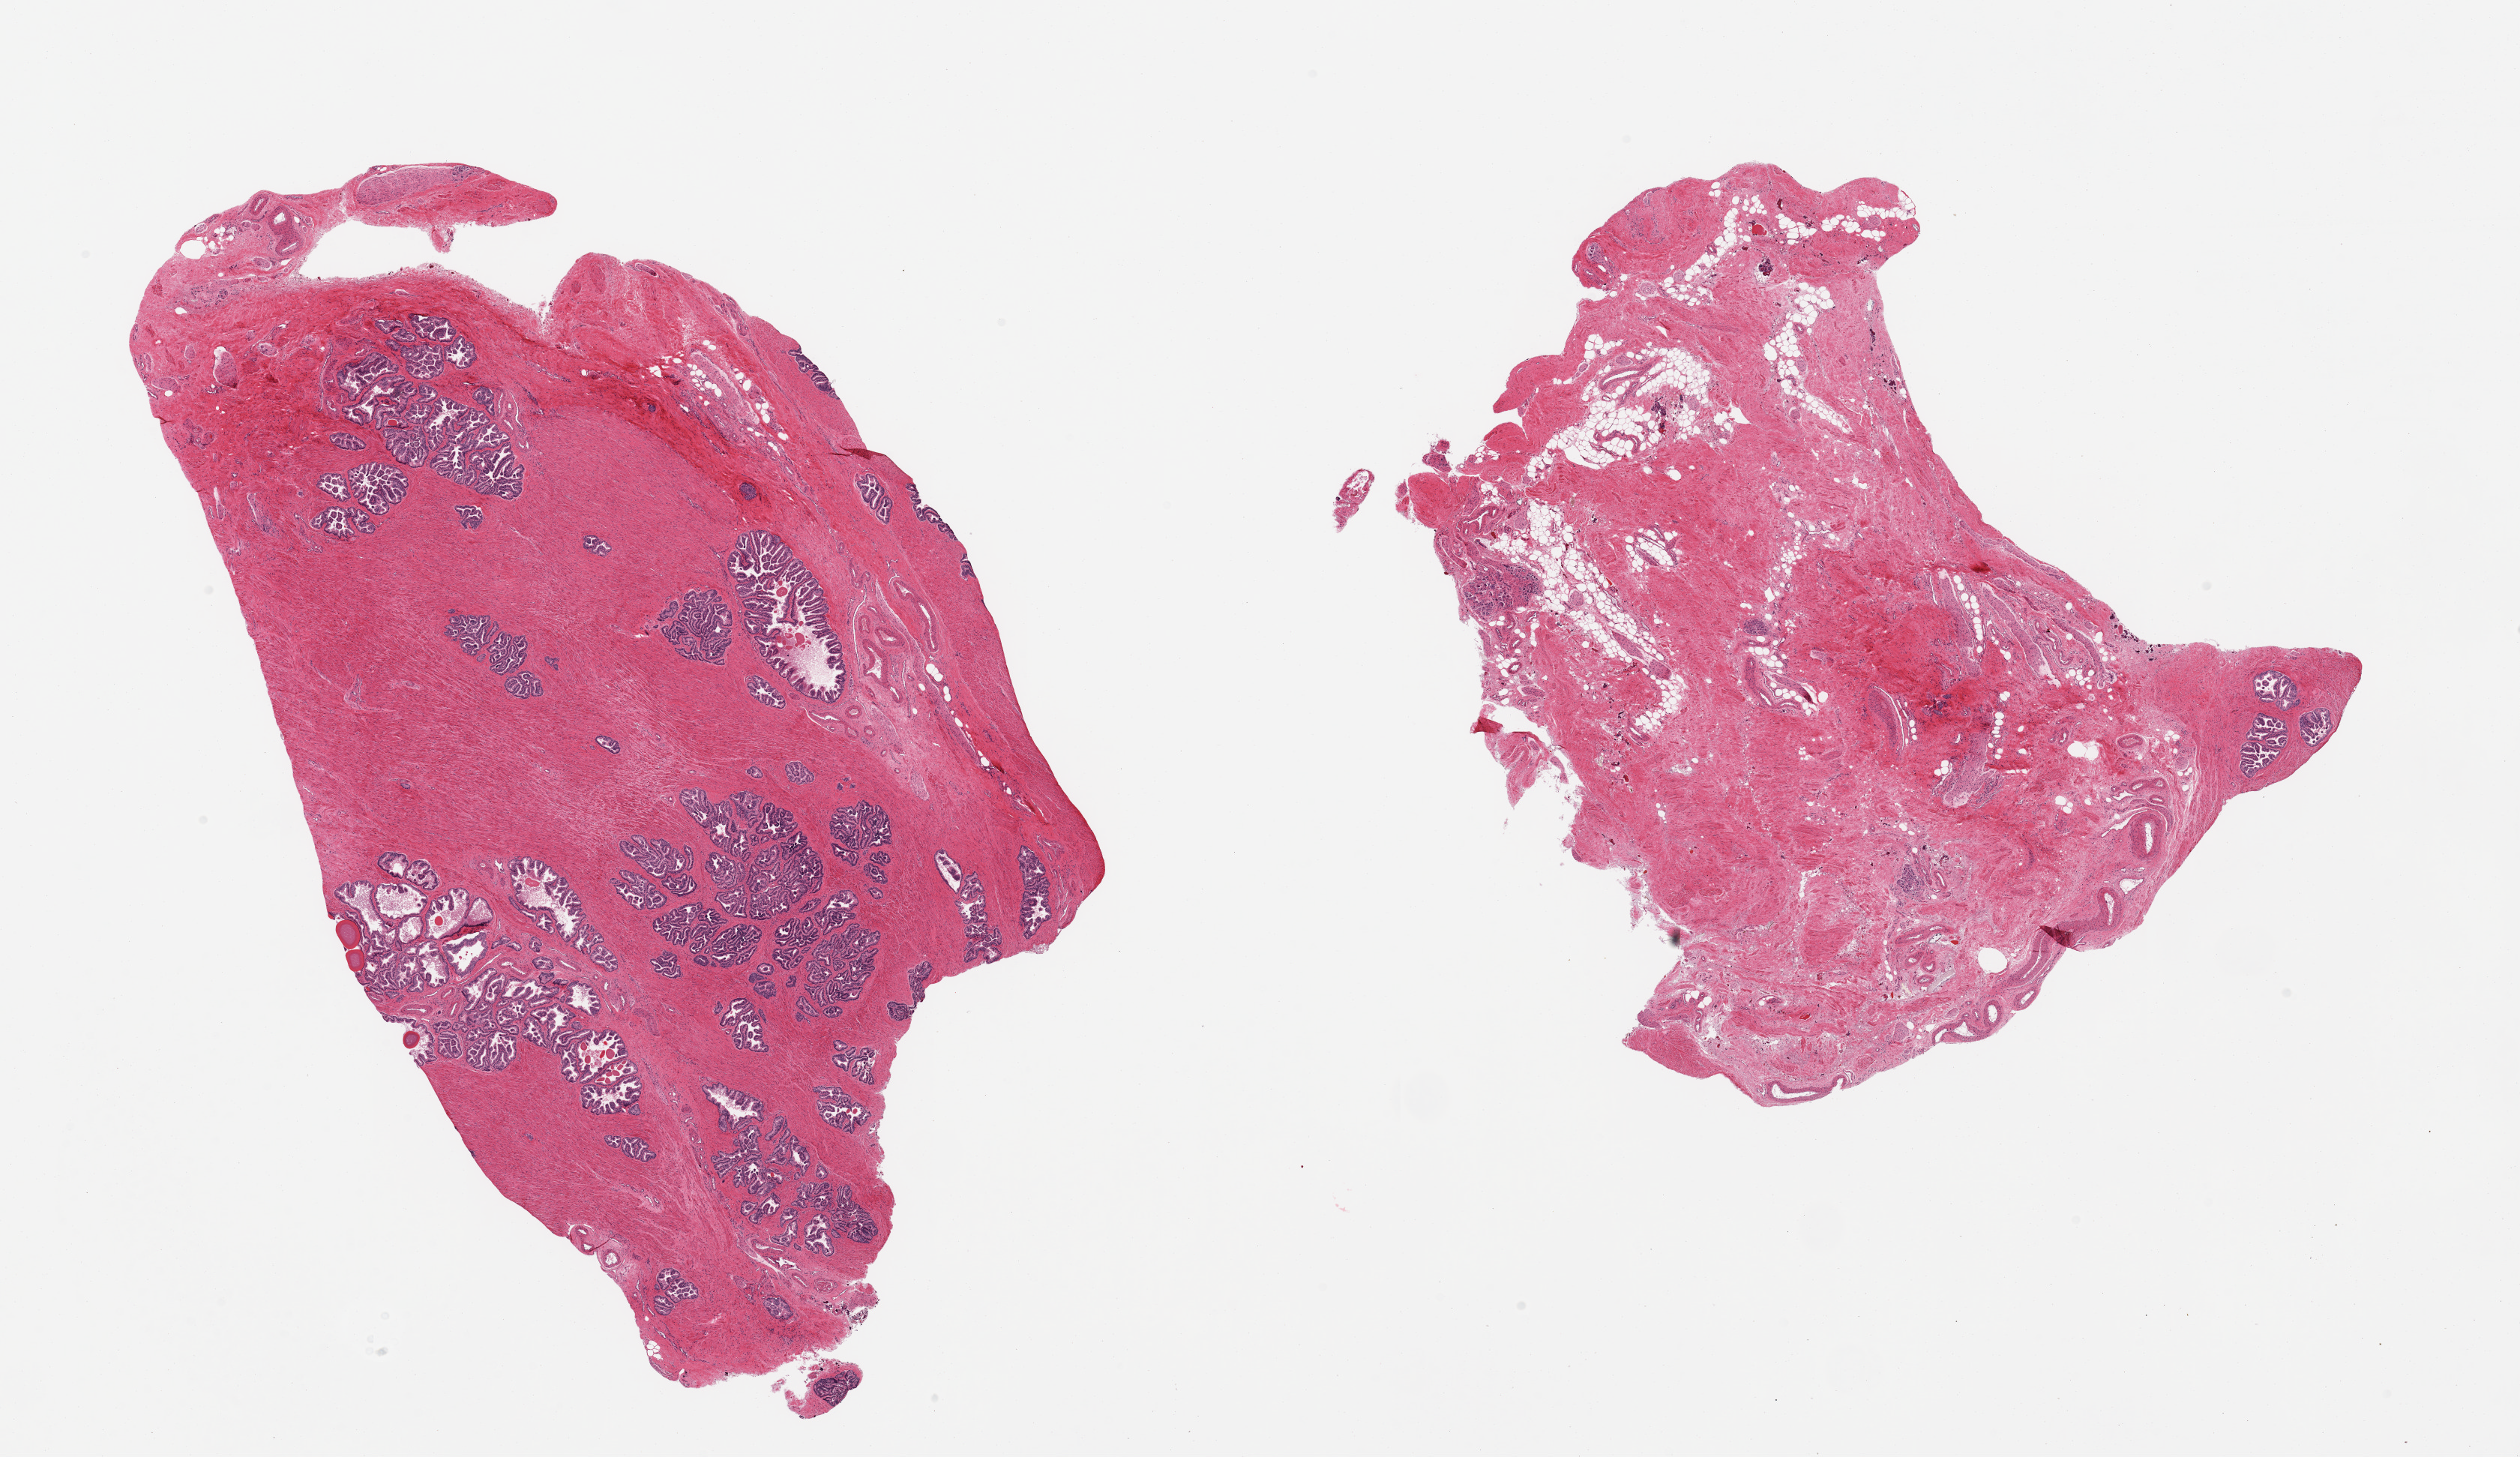
Whole-slide image, H&E stain — low-resolution overview of the scanned area, about 26.6 x 15.4 mm (from a 20x scan); PAXgene-fixed paraffin-embedded (PFPE) section; target tissue: prostate; tissue donor sample. Donor: male.
Review note (as recorded): 2 pieces; 1 piece has abundant well preserved prostatic tissue, other is 95% neuromuscular & fatty tissue.